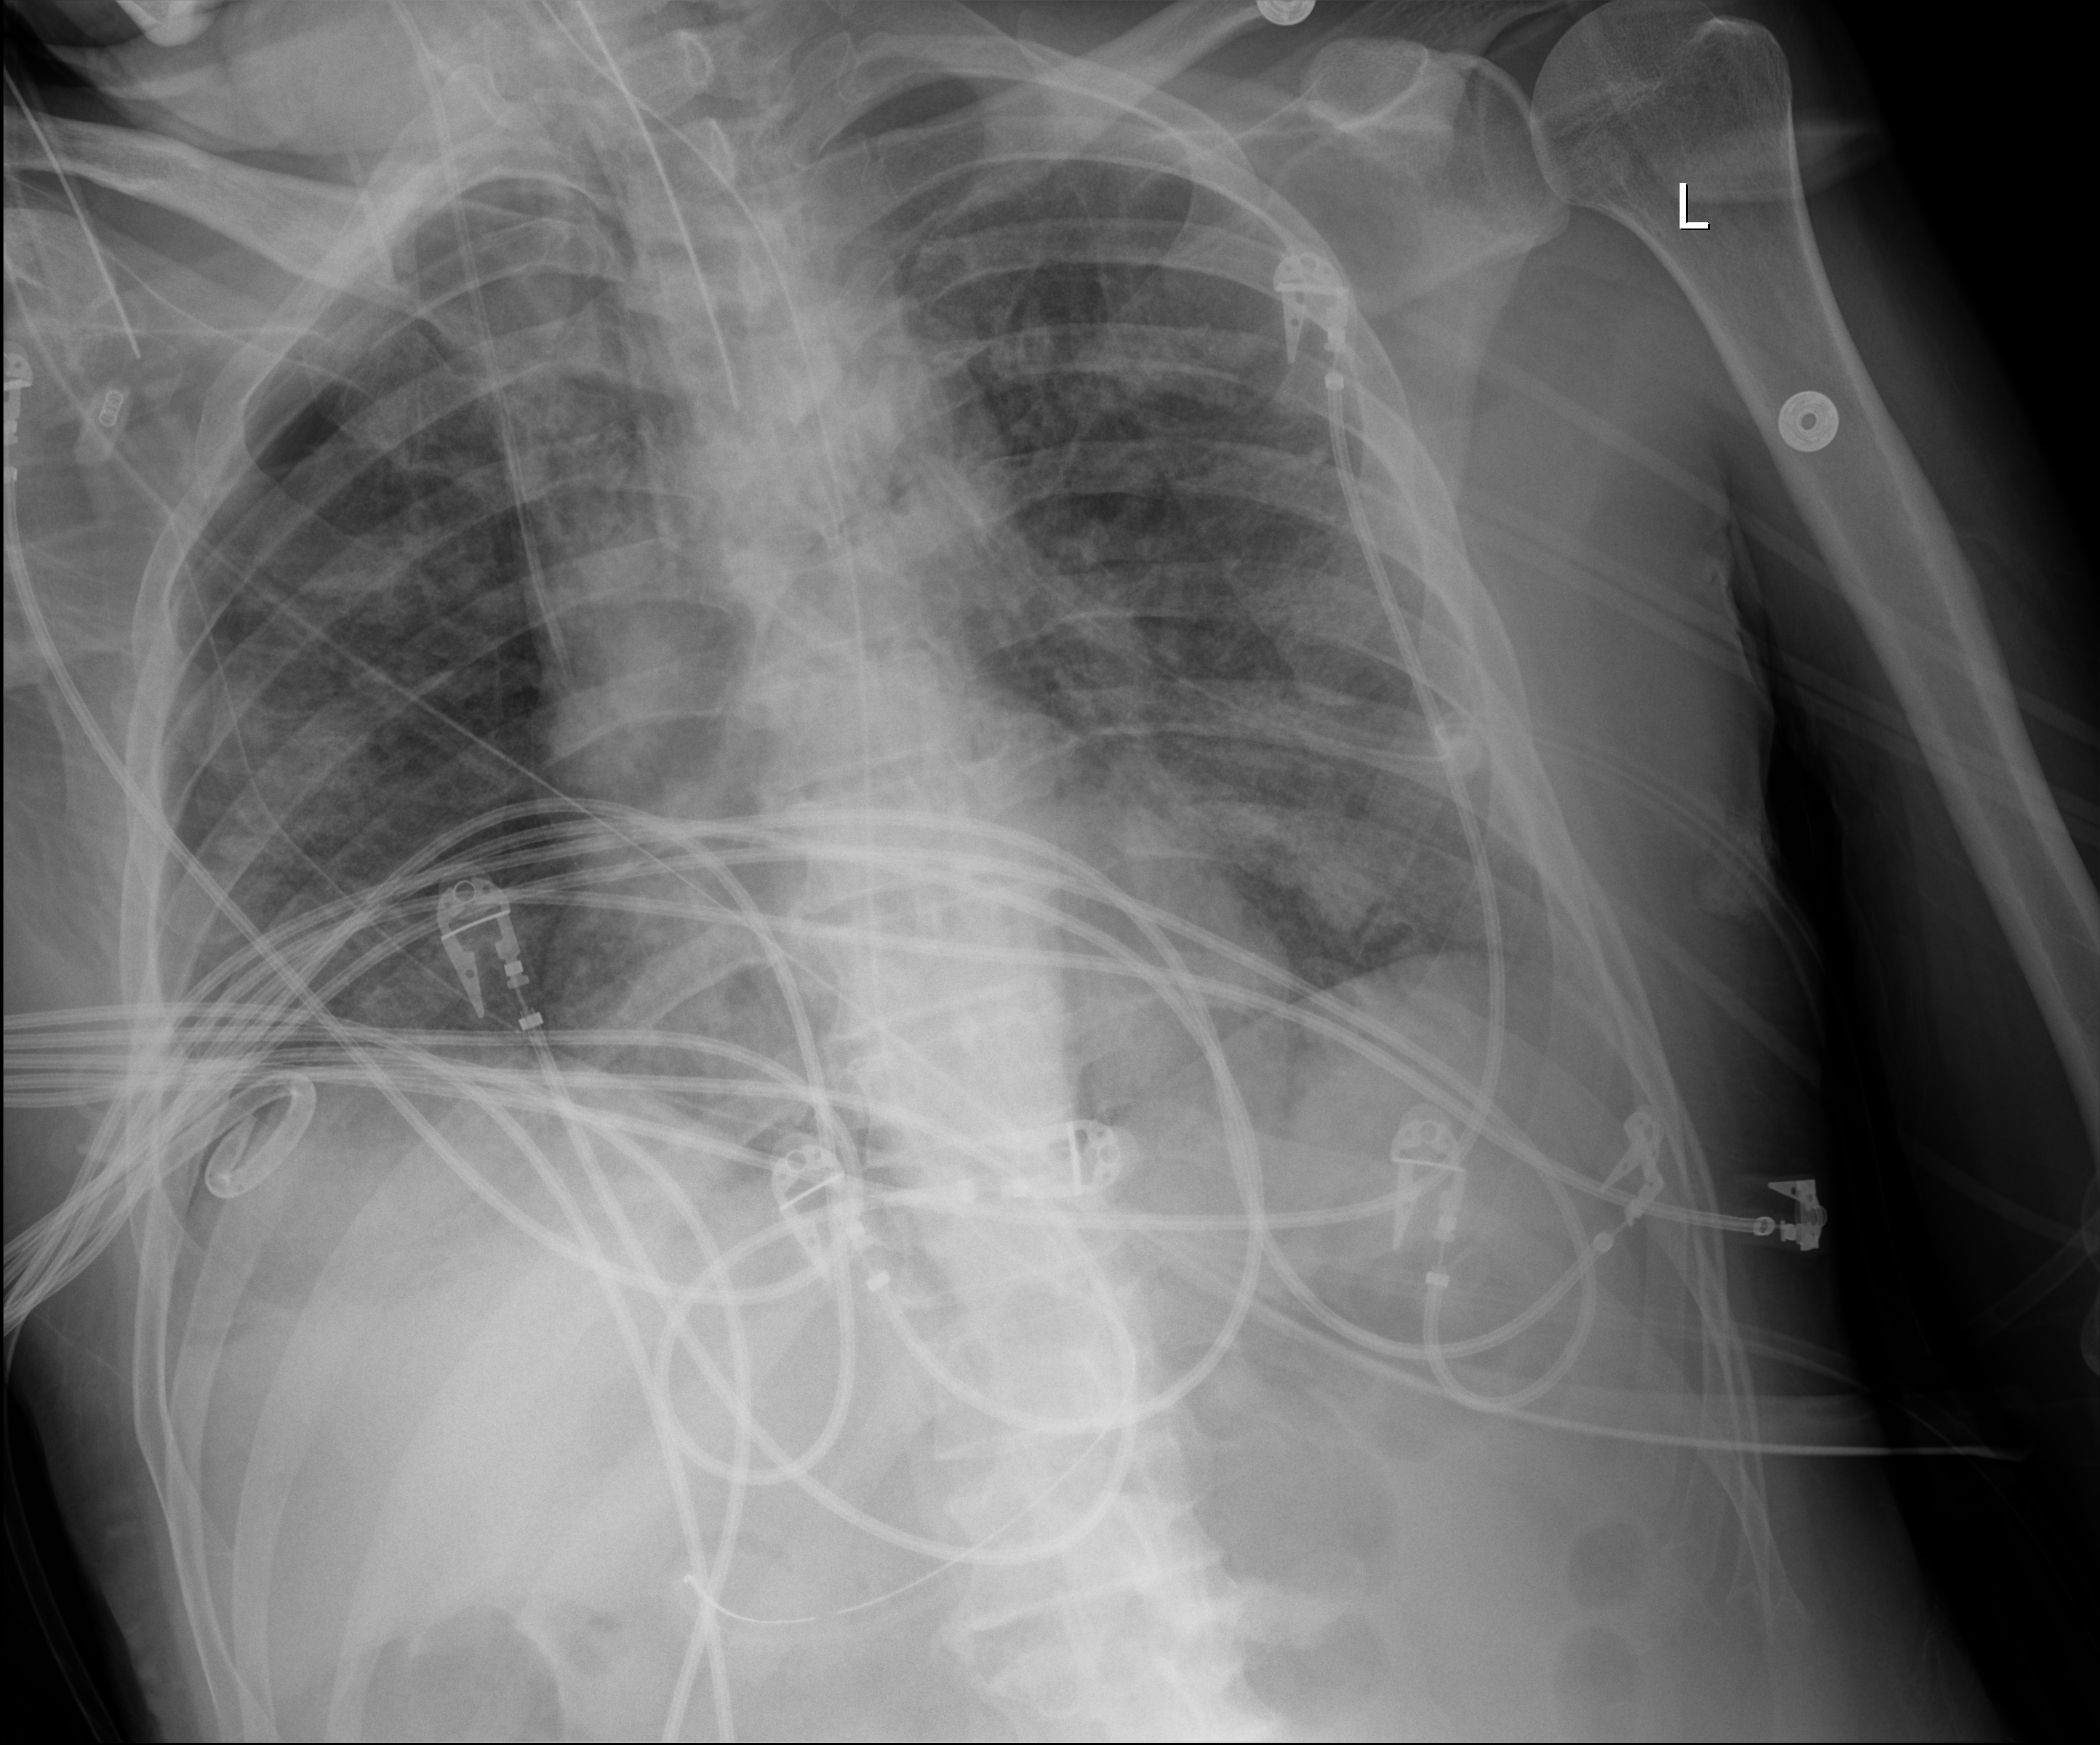
Bedside chest radiograph (digital radiography); anteroposterior (AP) projection. Male patient hospitalised with COVID-19, age 18–59 years.
From the hospital-stay record, not from the radiograph (when in the stay this image was taken is not recorded): other chronic lung disease (admission record): no; COPD (admission record): no.